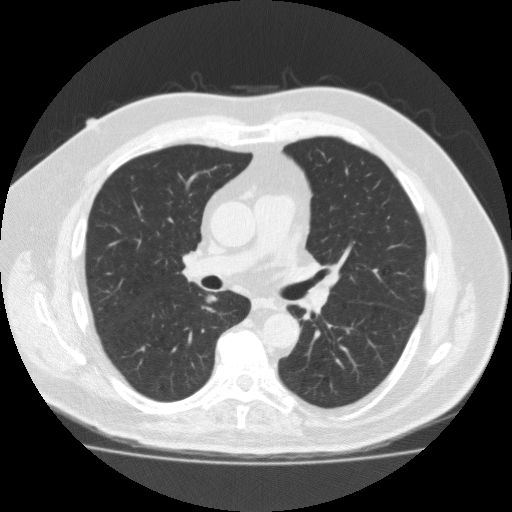
Chest CT (low-dose screening protocol), one axial image. Third annual screen. Lung window (W 1500 / L -600 HU). 2 mm slice thickness. Slice 74 of 183 in the series. Male participant, aged 56 years at enrolment. Current smoker at enrolment.
• Expert-annotated lung lesion, bounding box <188,282,229,317> (left, top, right, bottom; pixels).
• Screening reader's record for this exam (one nodule recorded; not confirmed to be the boxed lesion): non-calcified nodule or mass ≥4 mm, right lower lobe, 12 × 8 mm, spiculated (stellate) margins, soft tissue attenuation, pre-existing on the prior screen: yes; interval growth: yes.
• Official screen result: positive, other.